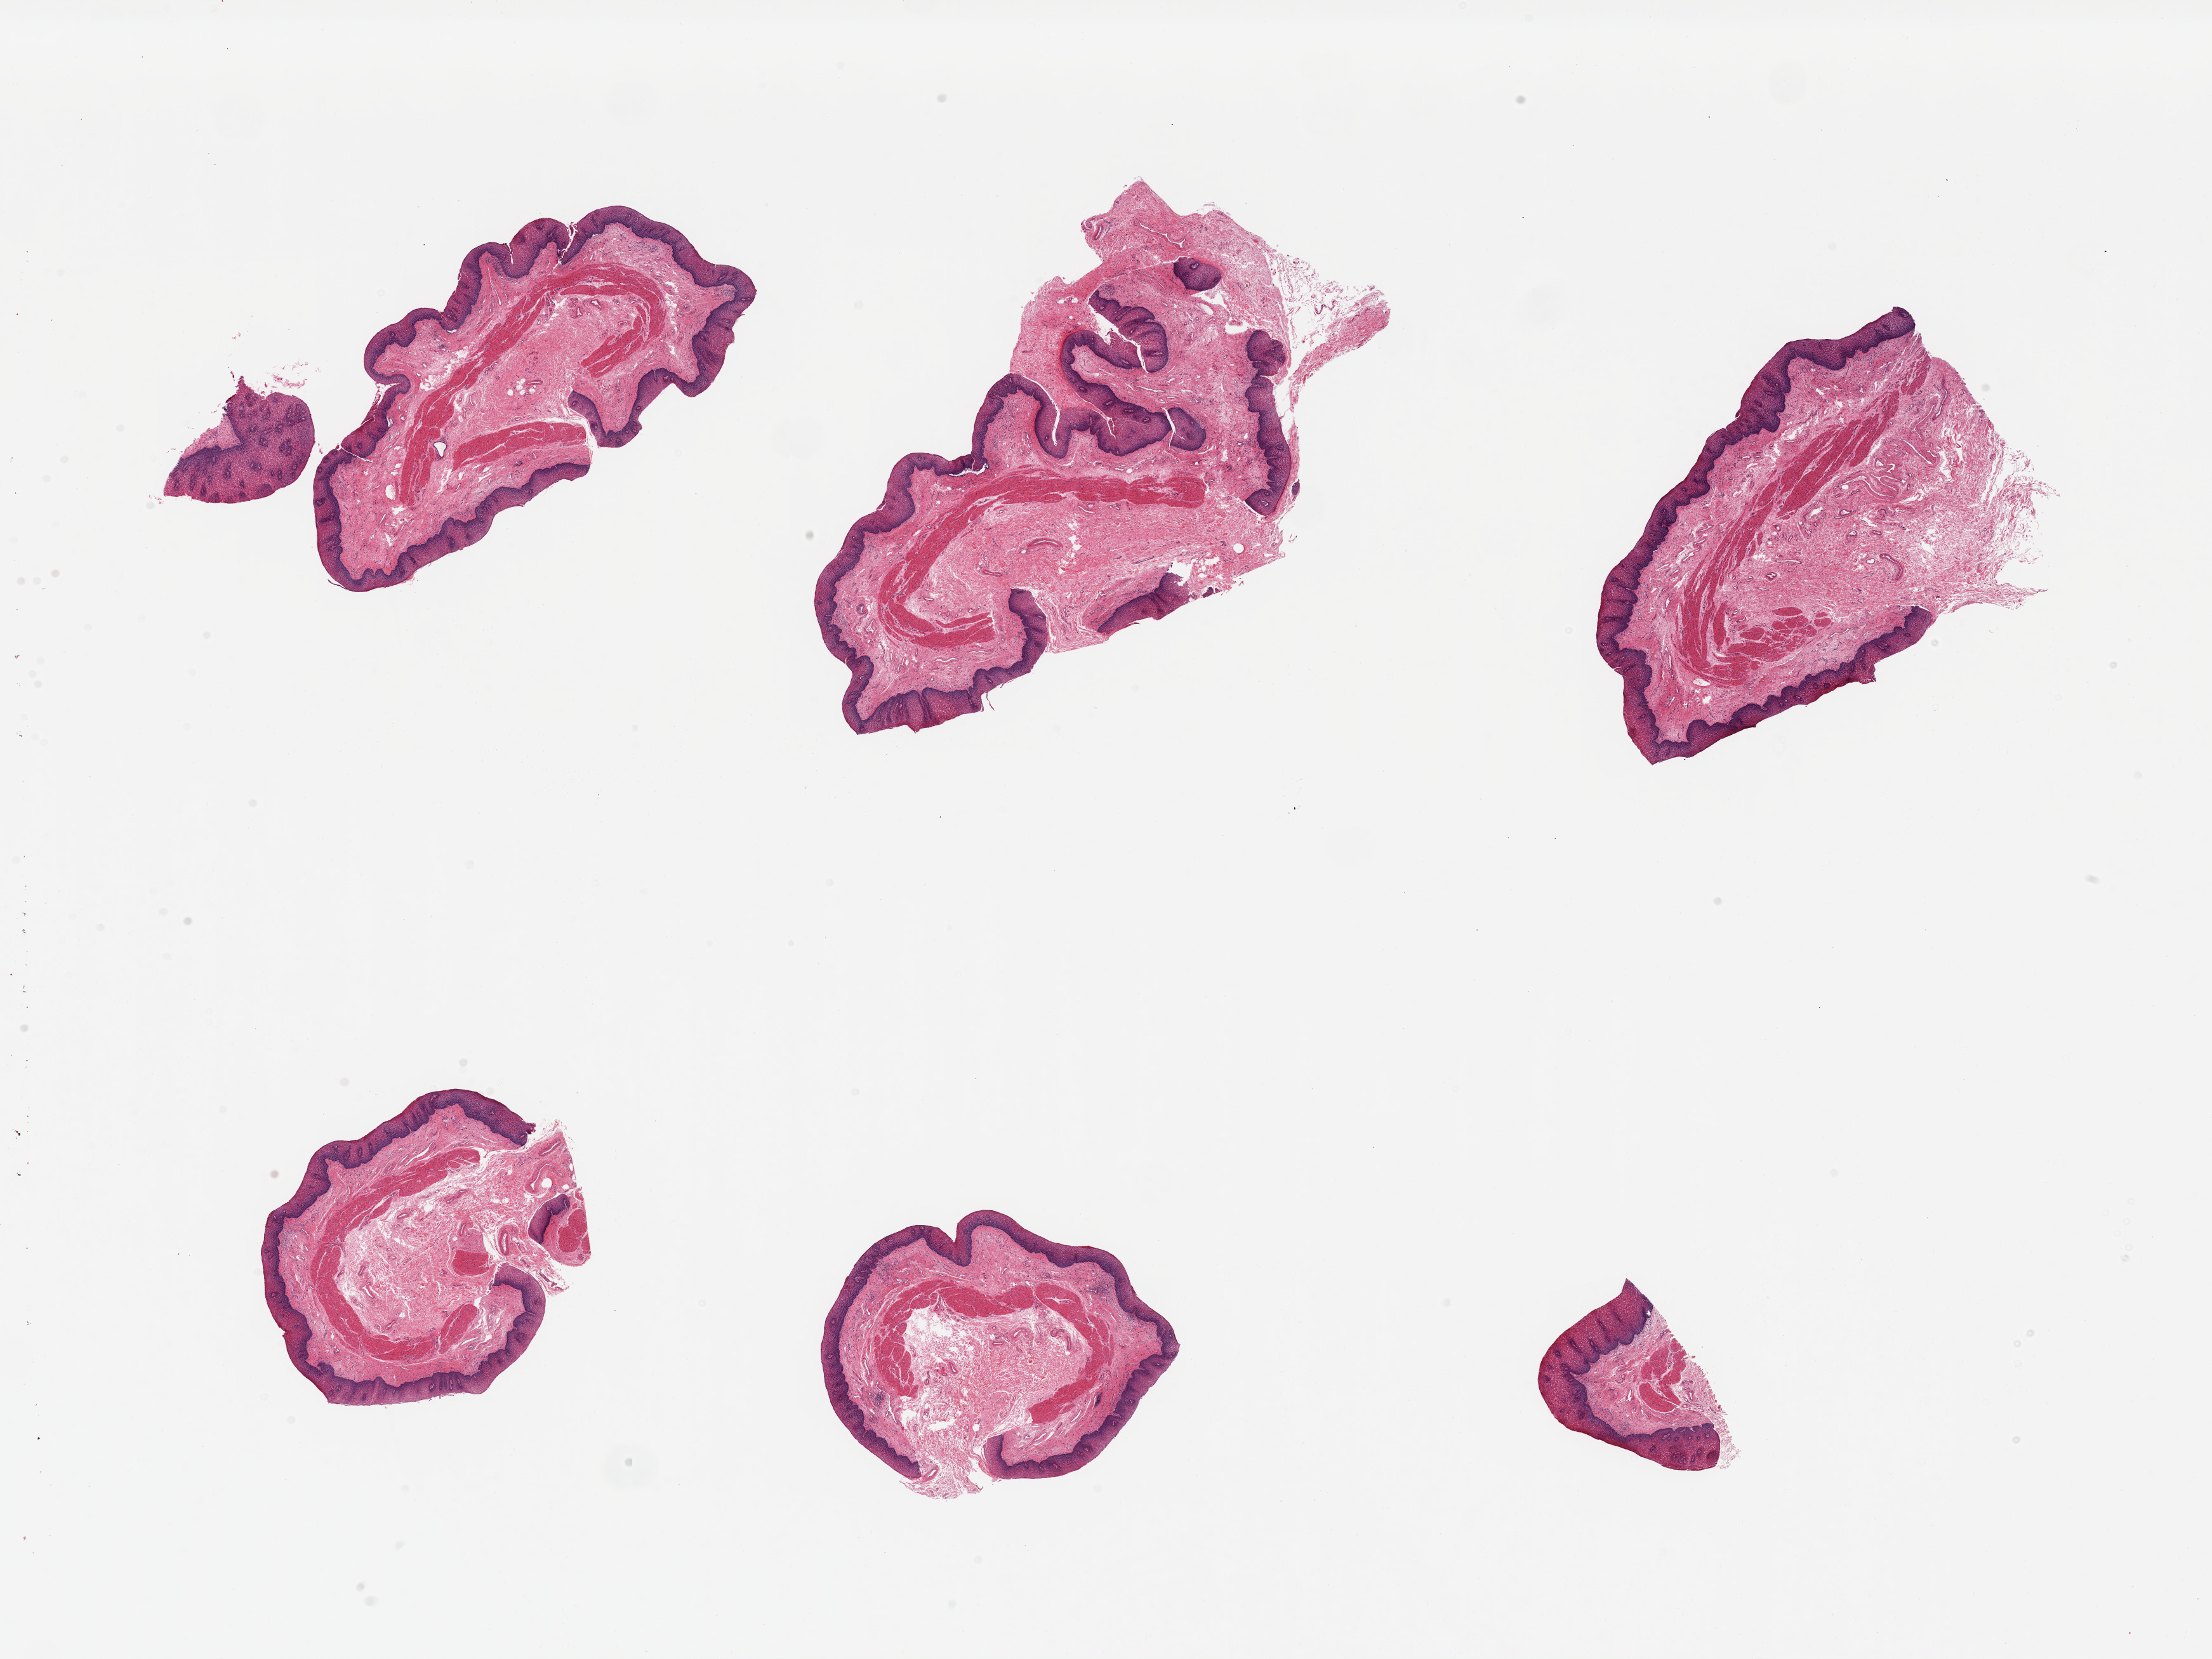
Whole-slide image, hematoxylin and eosin (H&E) stain — low-resolution overview of the scanned area, about 27.6 x 20.7 mm, PAXgene-fixed, paraffin-embedded tissue, target tissue: esophageal mucous membrane, tissue donor sample.
Pathologist's review note for this sample: 6 pieces; well preserved, well dissected mucosa.